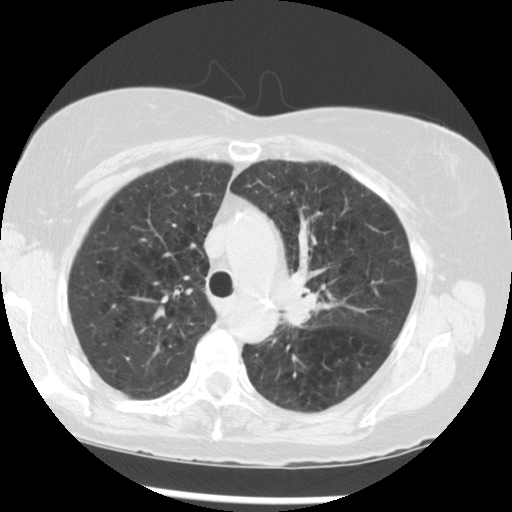
Chest CT (low-dose screening protocol), one axial image, third screening round (two years after baseline), lung window (W 1500 / L -600 HU), 2.5 mm slice thickness, standard (soft-tissue) reconstruction kernel (STANDARD). Female, age 70 years at enrolment. Current smoker at enrolment.
Lesion marked by an expert reader, bounding box (x1, y1, x2, y2) in pixels: (270, 261, 363, 351). The exam's reader record, not a measurement of the box and not confirmed to be the same lesion: non-calcified nodule or mass ≥4 mm, left upper lobe, 32 × 26 mm, spiculated (stellate) margins, soft tissue attenuation, pre-existing on the prior screen: yes; interval growth: yes. Official screen result: positive, other. Later outcome: lung cancer diagnosed 24 days after this screen — neoplasm, malignant, left upper lobe, stage IIIB (AJCC 6th edition), 40 mm at pathology.